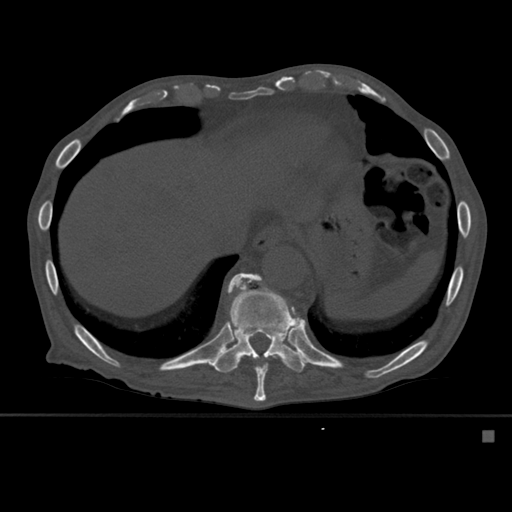
CT including the spine, one axial slice. Bone window (W 1800 / L 400 HU). 512 × 512 image matrix, field of view 373 × 373 mm. Patient: male, 78 years. From the clinical record (not read from this slice): primary cancer: prostate.
Structures marked on this image (semi-automatic segmentation, software-assisted and operator-edited):
- T10 vertebra: box from (x=230, y=273) to (x=296, y=402) px
- T11 vertebra: (x=212, y=273)–(x=309, y=373)